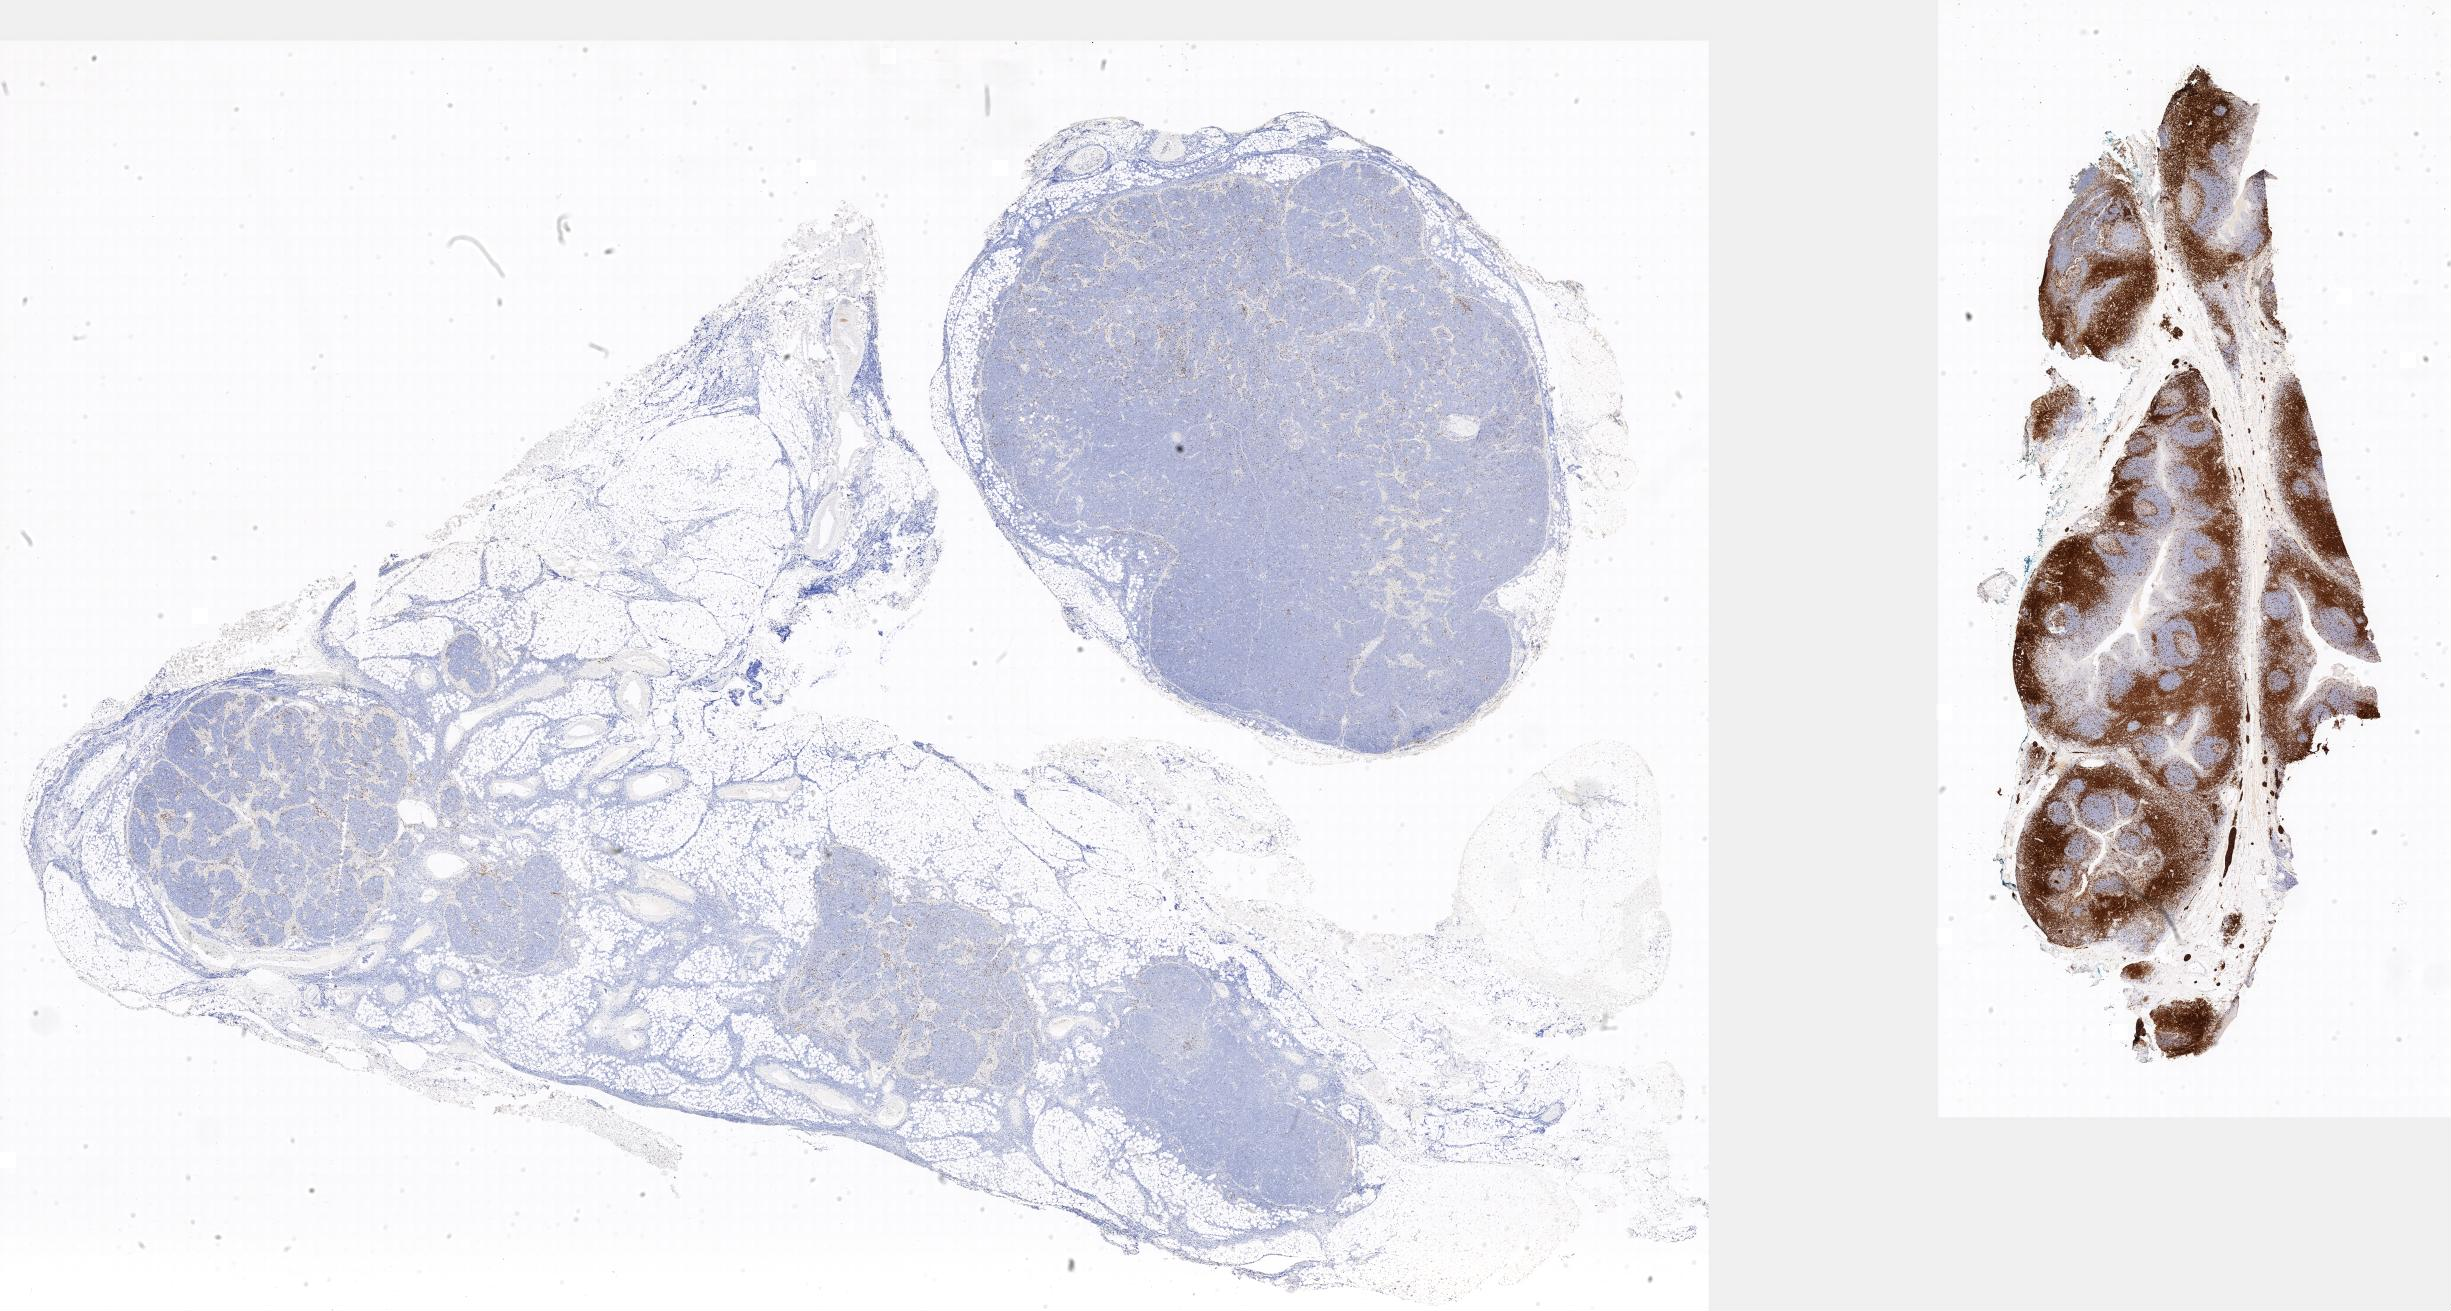
Whole-slide image, immunohistochemical stain for CD3, a low-resolution overview of the entire scanned area. Specimen: tumor tissue. Site: spleen. Female patient, aged 15.
Diagnosis: Burkitt lymphoma, NOS.